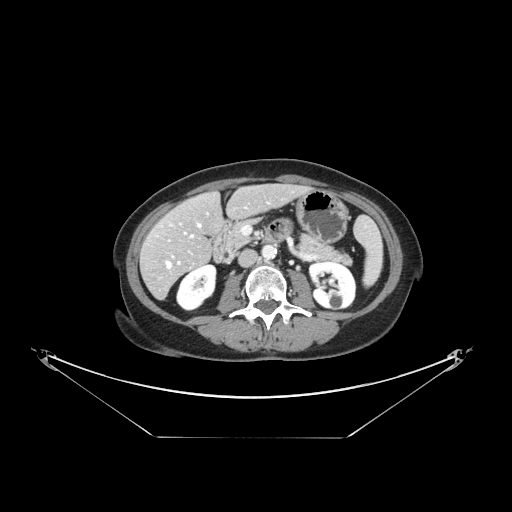
Contrast-enhanced abdominal CT, one axial slice; slice 56 of 148 in the series (ordered by position); reconstruction kernel STANDARD; 120 kVp; soft-tissue window (W 400 / L 40 HU); 2.5 mm slice thickness; 512 × 512 image matrix, field of view 500 × 500 mm. Female patient, age 73 years. Case-level facts recorded for this patient, not image findings: diagnosis: colorectal cancer liver metastases, imaged before liver resection; multiple liver metastases: no; largest metastasis: 1 cm; disease in both lobes: no.
Structures marked on this image (outlined manually by an expert reader):
- hepatic veins: bounding box <166,224,201,268> (left, top, right, bottom; pixels)
- liver: <142,185,304,298>
- planned liver remnant (the part of the liver to remain after resection): <164,185,304,248>